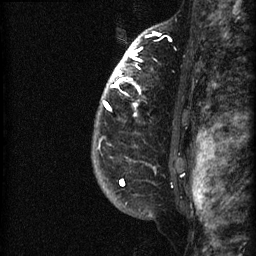
Breast MRI (dynamic contrast-enhanced), one sagittal slice; position 55 of 60 along the scan axis; dynamic contrast-enhanced series, image 2 of 3 at this slice position (ordered by acquisition); 1.5 T; TE 4.2 ms, TR 22.7 ms; 256 × 256 image matrix, field of view 180 × 180 mm. Female patient, age 48 years. Case-level facts recorded for this patient, not image findings: setting: breast cancer imaged before/during neoadjuvant chemotherapy; receptor status: triple-negative.
Structures marked on this image (semi-automatically segmented with operator editing):
- analysis volume of interest (the breast-tissue region the enhancement analysis was run in; not a lesion): bounding box (x1, y1, x2, y2) in pixels: (92, 27, 191, 180)
- tumour enhancement mask (voxels above the 90 % enhancement threshold inside the analysis volume of interest): (103, 32, 157, 180)